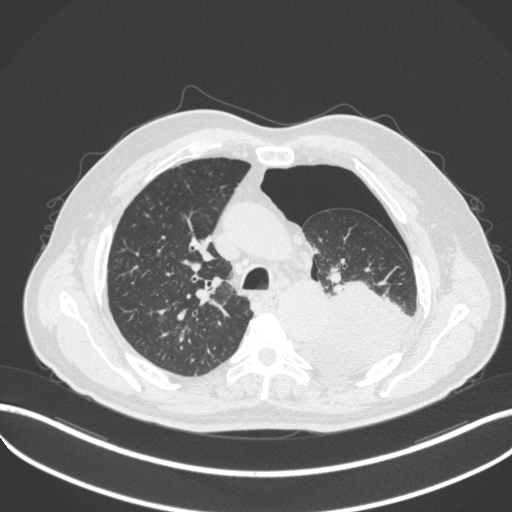
Chest CT, one axial slice. Slice 358 of 466 in the series (ordered by position). Reconstruction kernel B31f. 120 kVp. Lung window (W 1500 / L -600 HU). 1 mm slice thickness. 512 × 512 image matrix. Patient: male, 76 years. Case-level facts recorded for this patient, not image findings: clinical TNM (as recorded): T3 N0 M1b.
Outlined on this slice (bounding box drawn by a radiologist):
- lung tumour (recorded histology: adenocarcinoma): bounding box (x1, y1, x2, y2) in pixels: (308, 275, 412, 379)